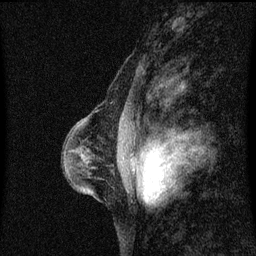
Breast MRI (dynamic contrast-enhanced), one sagittal slice. Slice 38 of 60 in the series (ordered by position). Dynamic contrast-enhanced series, image 2 of 3 at this slice position (ordered by acquisition). 1.5 T. TE 4.2 ms, TR 8.4 ms. 2 mm slice thickness. 256 × 256 image matrix. Female patient, age 41 years. From the clinical record (not read from this slice): setting: breast cancer imaged before/during neoadjuvant chemotherapy; receptor status: triple-negative.
Annotated regions visible in this slice (semi-automatic segmentation, software-assisted and operator-edited):
- analysis volume of interest (the breast-tissue region the enhancement analysis was run in; not a lesion): box from (x=64, y=124) to (x=135, y=201) px
- tumour enhancement mask (voxels above the 70 % enhancement threshold inside the analysis volume of interest): (x=122, y=158)–(x=135, y=163)